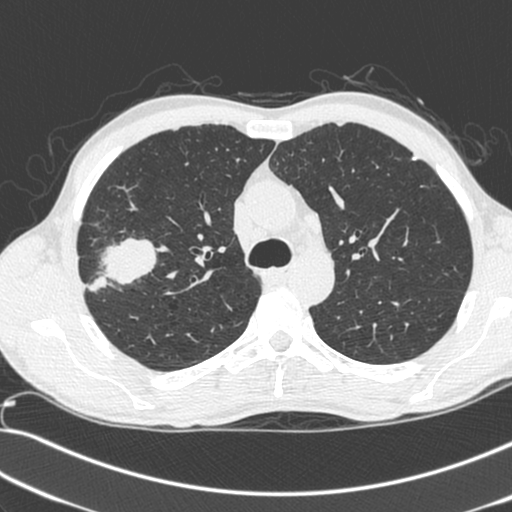
Chest CT (low-dose screening protocol), one axial image; baseline screening round; lung window (W 1500 / L -600 HU); 1.3 mm slice thickness; 120 kVp; slice 75 of 281 in the series. Male participant, aged 55 years at enrolment. Current smoker at enrolment.
Expert-annotated lung lesion, bounding box (x1, y1, x2, y2) in pixels: (71, 234, 151, 307). Reader record for this screening exam (exam-level; its link to the box is not recorded): non-calcified nodule or mass ≥4 mm, right upper lobe, 52 × 39 mm, spiculated (stellate) margins, soft tissue attenuation. Later outcome: lung cancer diagnosed 25 days after this screen — large cell neuroendocrine carcinoma, right upper lobe, poorly differentiated (G3), stage IIB (AJCC 6th edition), 49 mm at pathology.